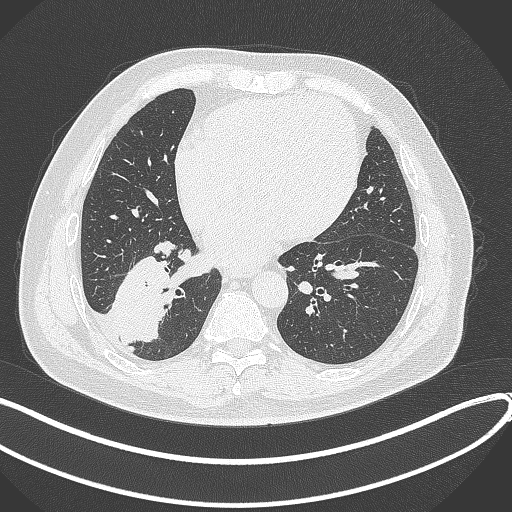
Chest CT, one axial slice. Position 133 of 360 along the scan axis. Reconstruction kernel B70f. 120 kVp. Lung window (W 1500 / L -600 HU). 1 mm slice thickness. 512 × 512 image matrix, field of view 400 × 400 mm. Male patient, age 59 years.
Outlined on this slice (rectangle marked by the reading radiologist):
- lung tumour (recorded histology: adenocarcinoma): bounding box <108,252,173,346> (left, top, right, bottom; pixels)